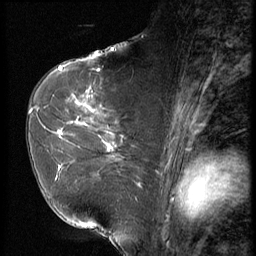
Breast MRI (dynamic contrast-enhanced), one sagittal slice. Position 38 of 56 along the scan axis. 3 images stored at this slice position (order not interpretable as contrast timing). 1.5 T. TE 4.2 ms, TR 9 ms. 2.5 mm slice thickness. 256 × 256 image matrix. Female patient, age 61 years. Case-level facts recorded for this patient, not image findings: setting: breast cancer imaged before/during neoadjuvant chemotherapy; receptor status: HR-positive, HER2-negative.
Annotated regions visible in this slice (semi-automatic segmentation, software-assisted and operator-edited):
- analysis volume of interest (the breast-tissue region the enhancement analysis was run in; not a lesion): bounding box [x1, y1, x2, y2] px = [47, 89, 153, 191]
- tumour enhancement mask (voxels above the 140 % enhancement threshold inside the analysis volume of interest): [56, 103, 112, 178]